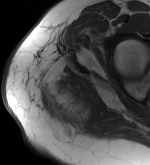
MRI of an extremity soft-tissue mass, one axial slice; slice 42 of 56 in the series (ordered by position); MR volume resampled by the dataset authors to the PET/CT grid (not the native acquisition matrix); 3.27 mm slice thickness; 150 × 165 image matrix, field of view 146 × 161 mm. Female patient. From the clinical record (not read from this slice): histological type: epithelioid sarcoma with vascular differentiation; site of the primary tumour: right buttock.
Annotated regions visible in this slice (expert contour drawn on MRI and transferred to this co-registered scan by the dataset authors):
- gross tumour volume (mass): box from (x=37, y=78) to (x=90, y=119) px